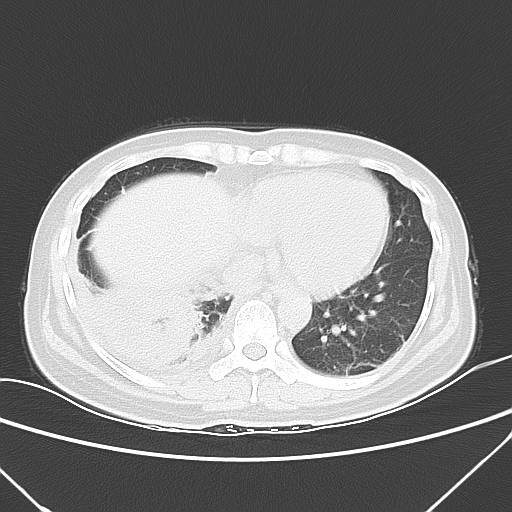
Chest CT, one axial slice; 120 kVp; lung window (W 1500 / L -600 HU); 5 mm slice thickness; 512 × 512 image matrix. Female patient, age 42 years. From the clinical record (not read from this slice): clinical TNM (as recorded): T3 N0 M1c.
Structures marked on this image (rectangle marked by the reading radiologist):
- lung tumour (recorded histology: adenocarcinoma): bounding box (x1, y1, x2, y2) in pixels: (79, 281, 202, 374)